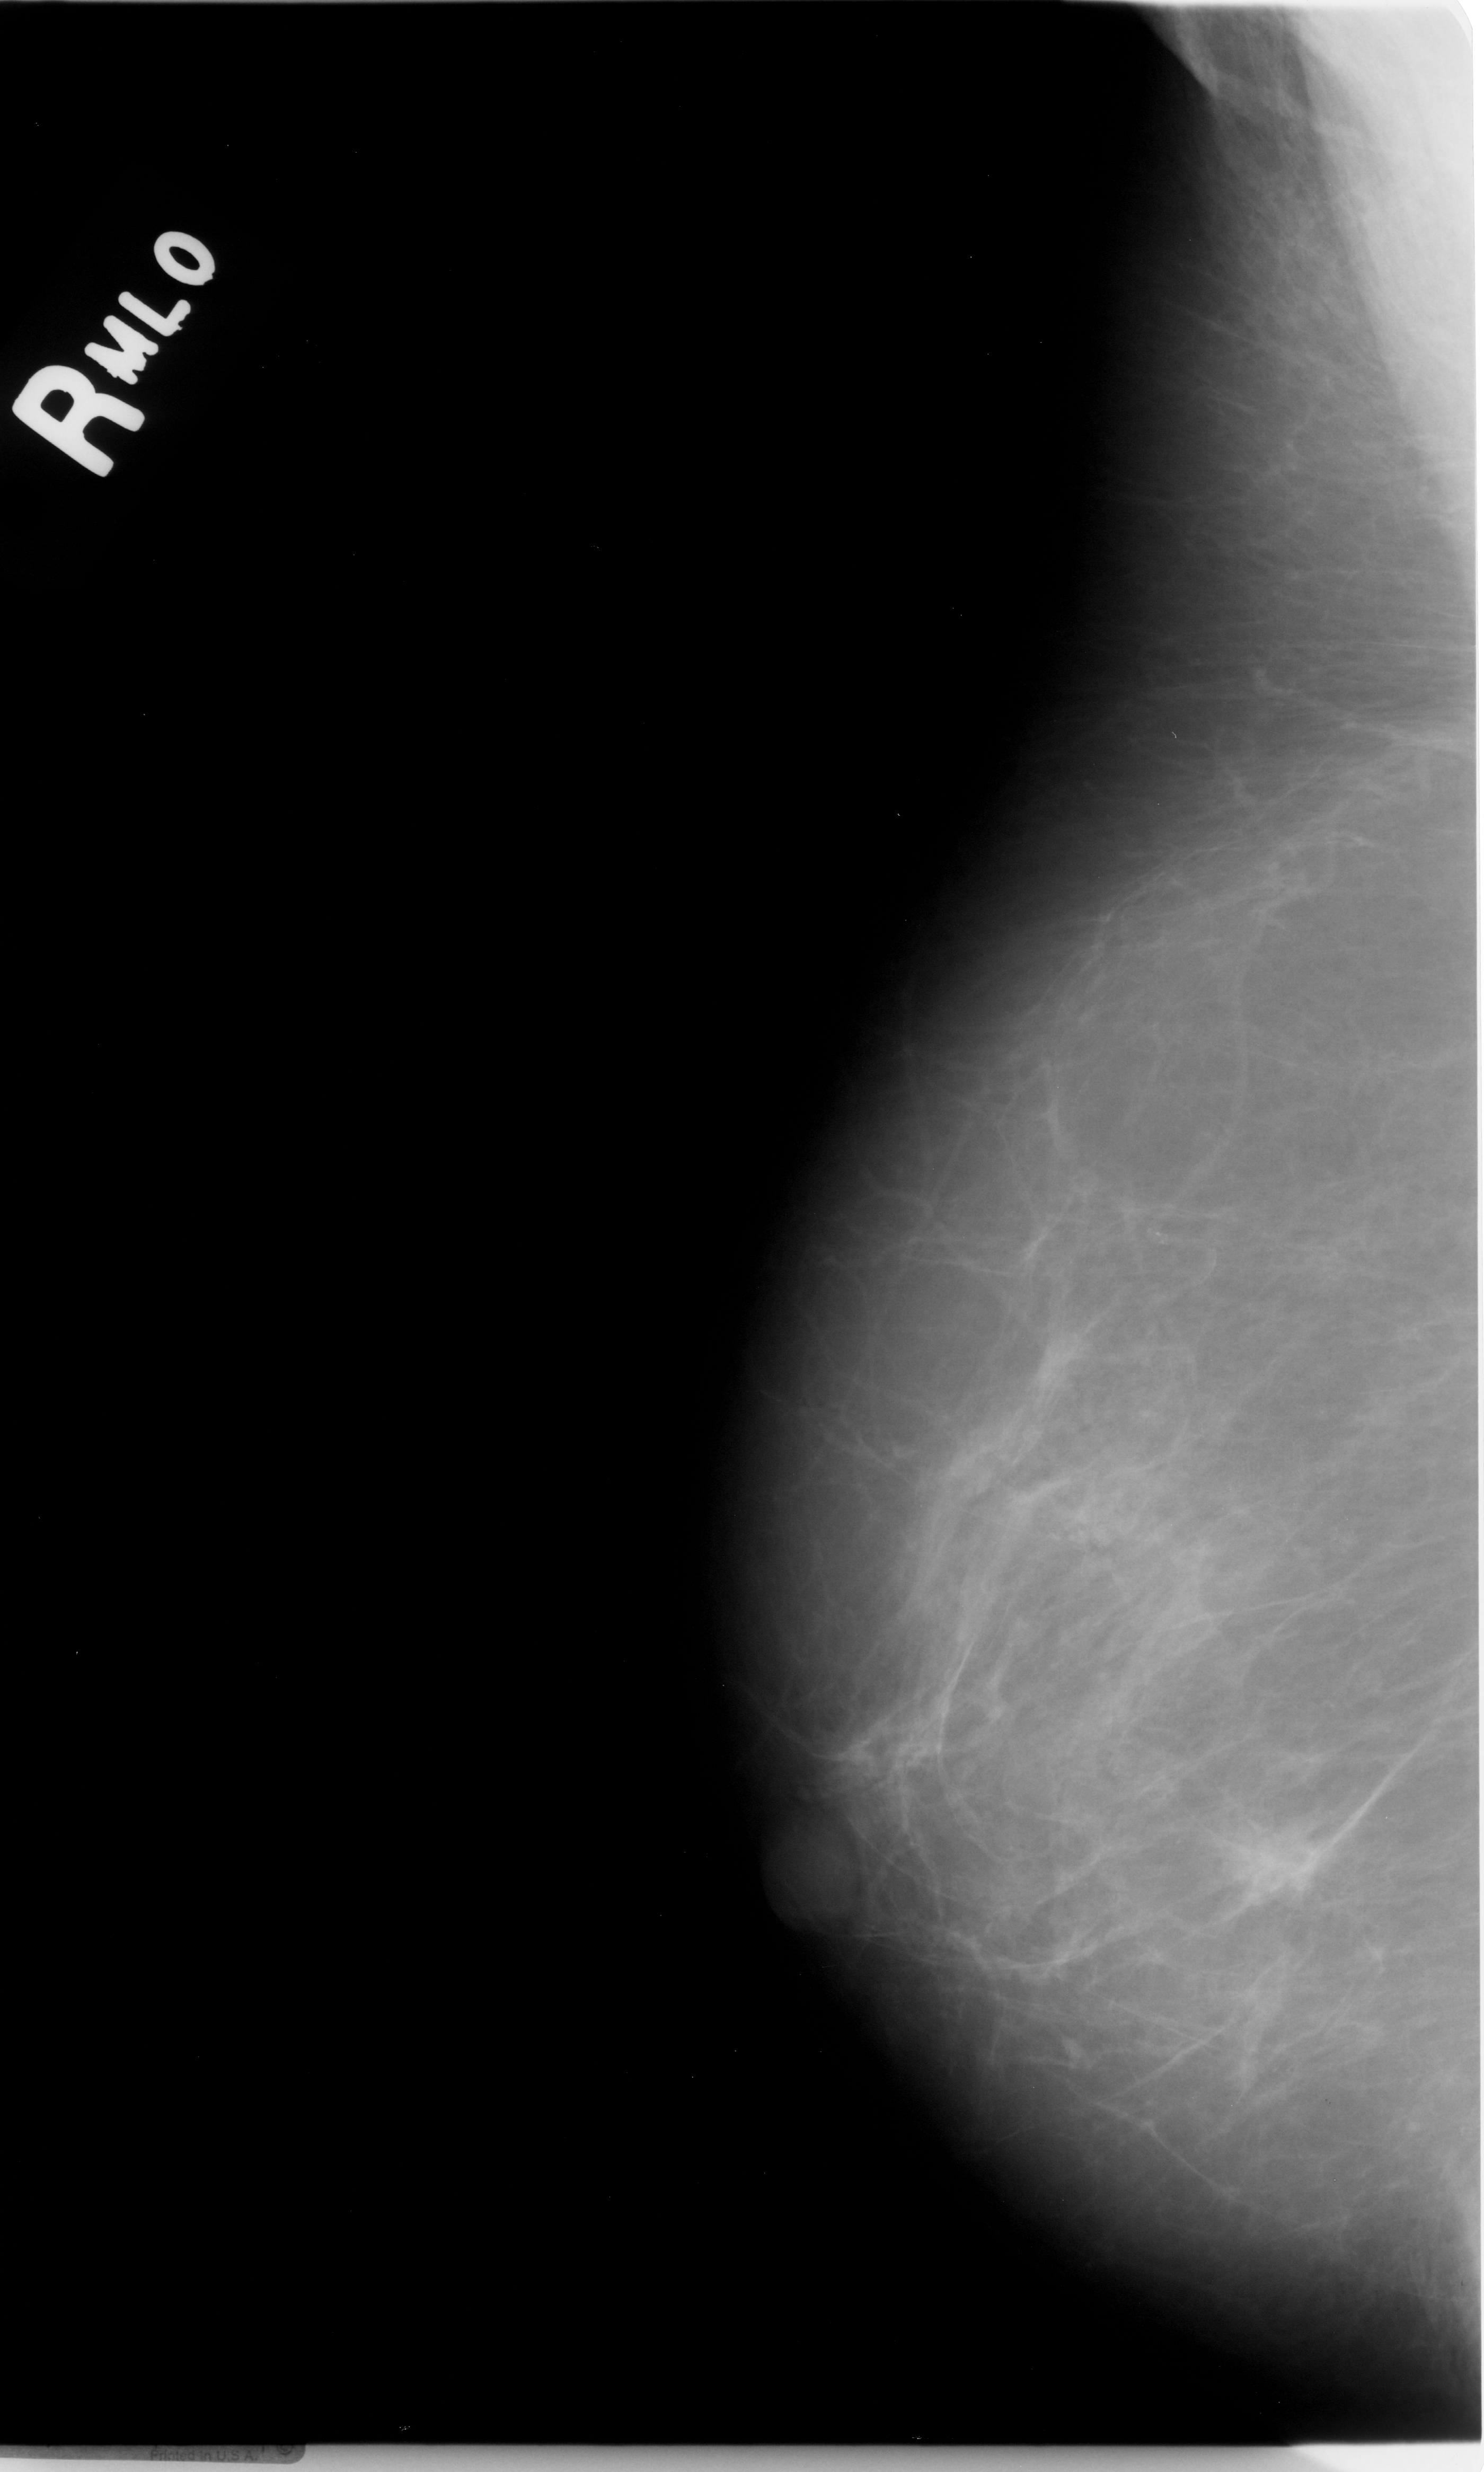
Scanned film-screen mammogram; right breast; MLO view; BI-RADS breast density category 1 (scale 1–4).
- Radiologist-marked abnormalities on this image: mass, shape irregular, margins microlobulated; BI-RADS assessment category 5; pathology result (as recorded, not read from the image): malignant.